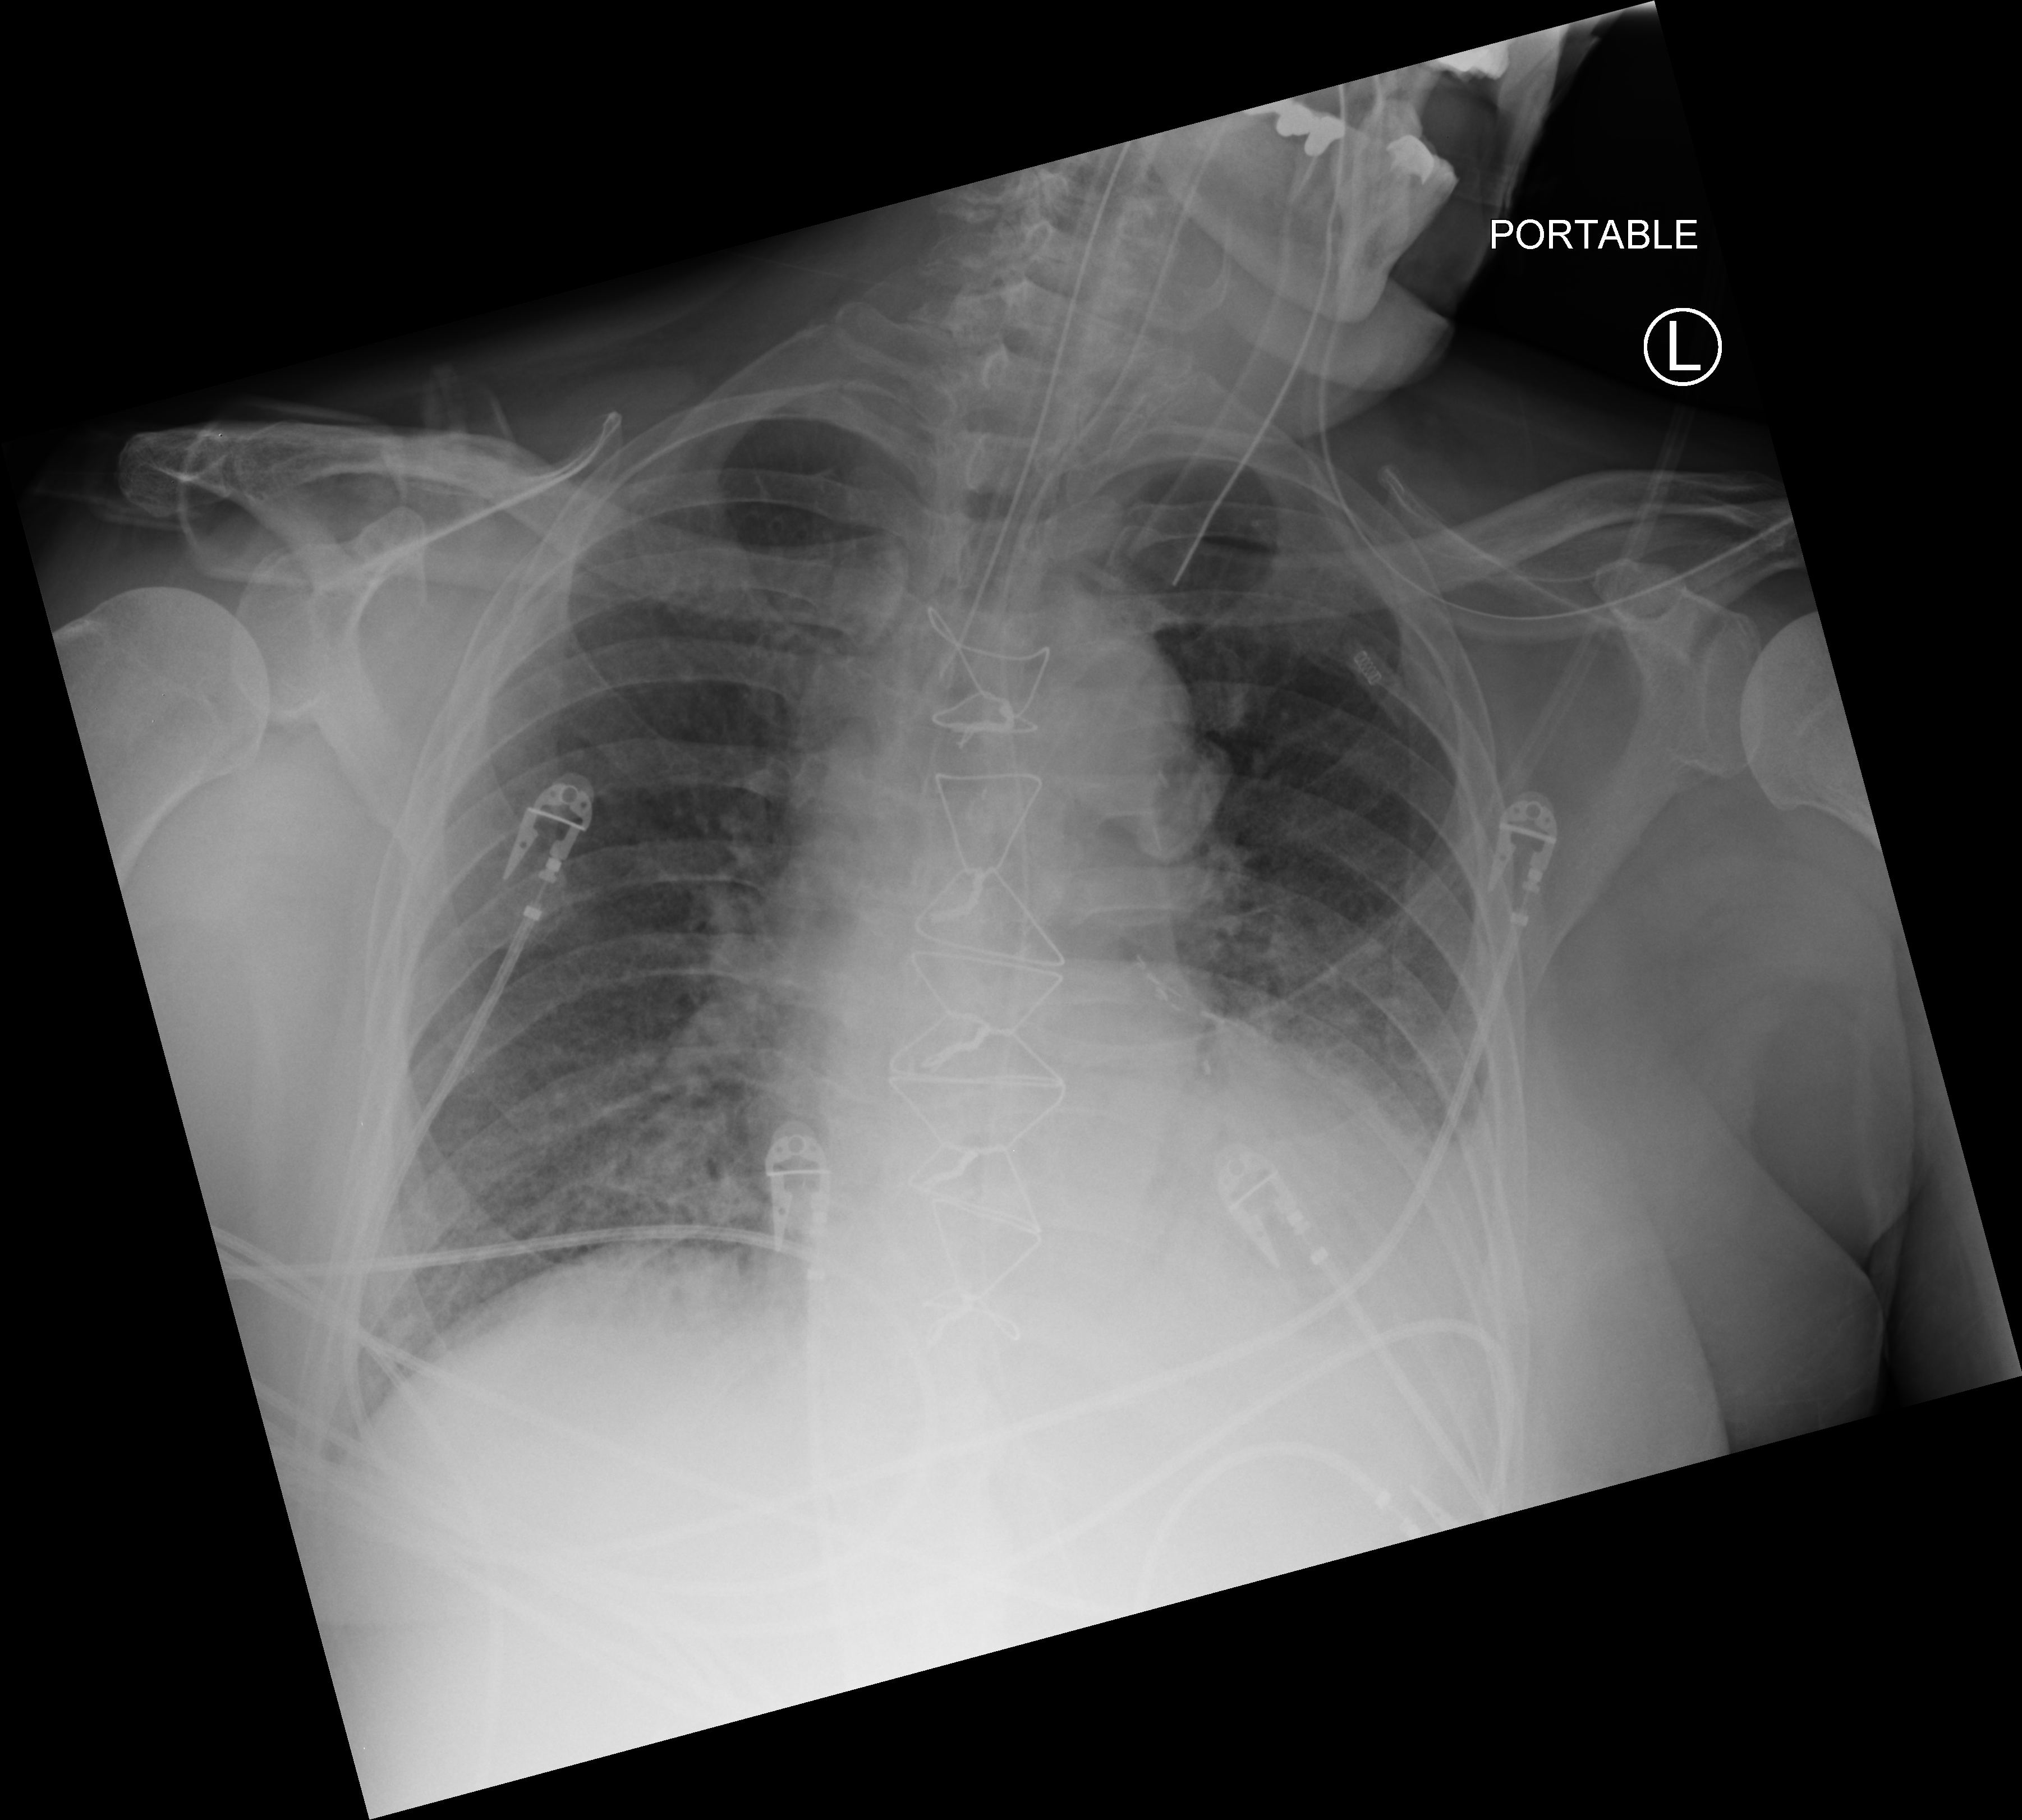
Chest X-ray (portable), anteroposterior (AP) projection. Patient hospitalised with COVID-19; male, aged 75–90 years.
From the hospital-stay record, not from the radiograph (when in the stay this image was taken is not recorded):
- other chronic lung disease (admission record): yes